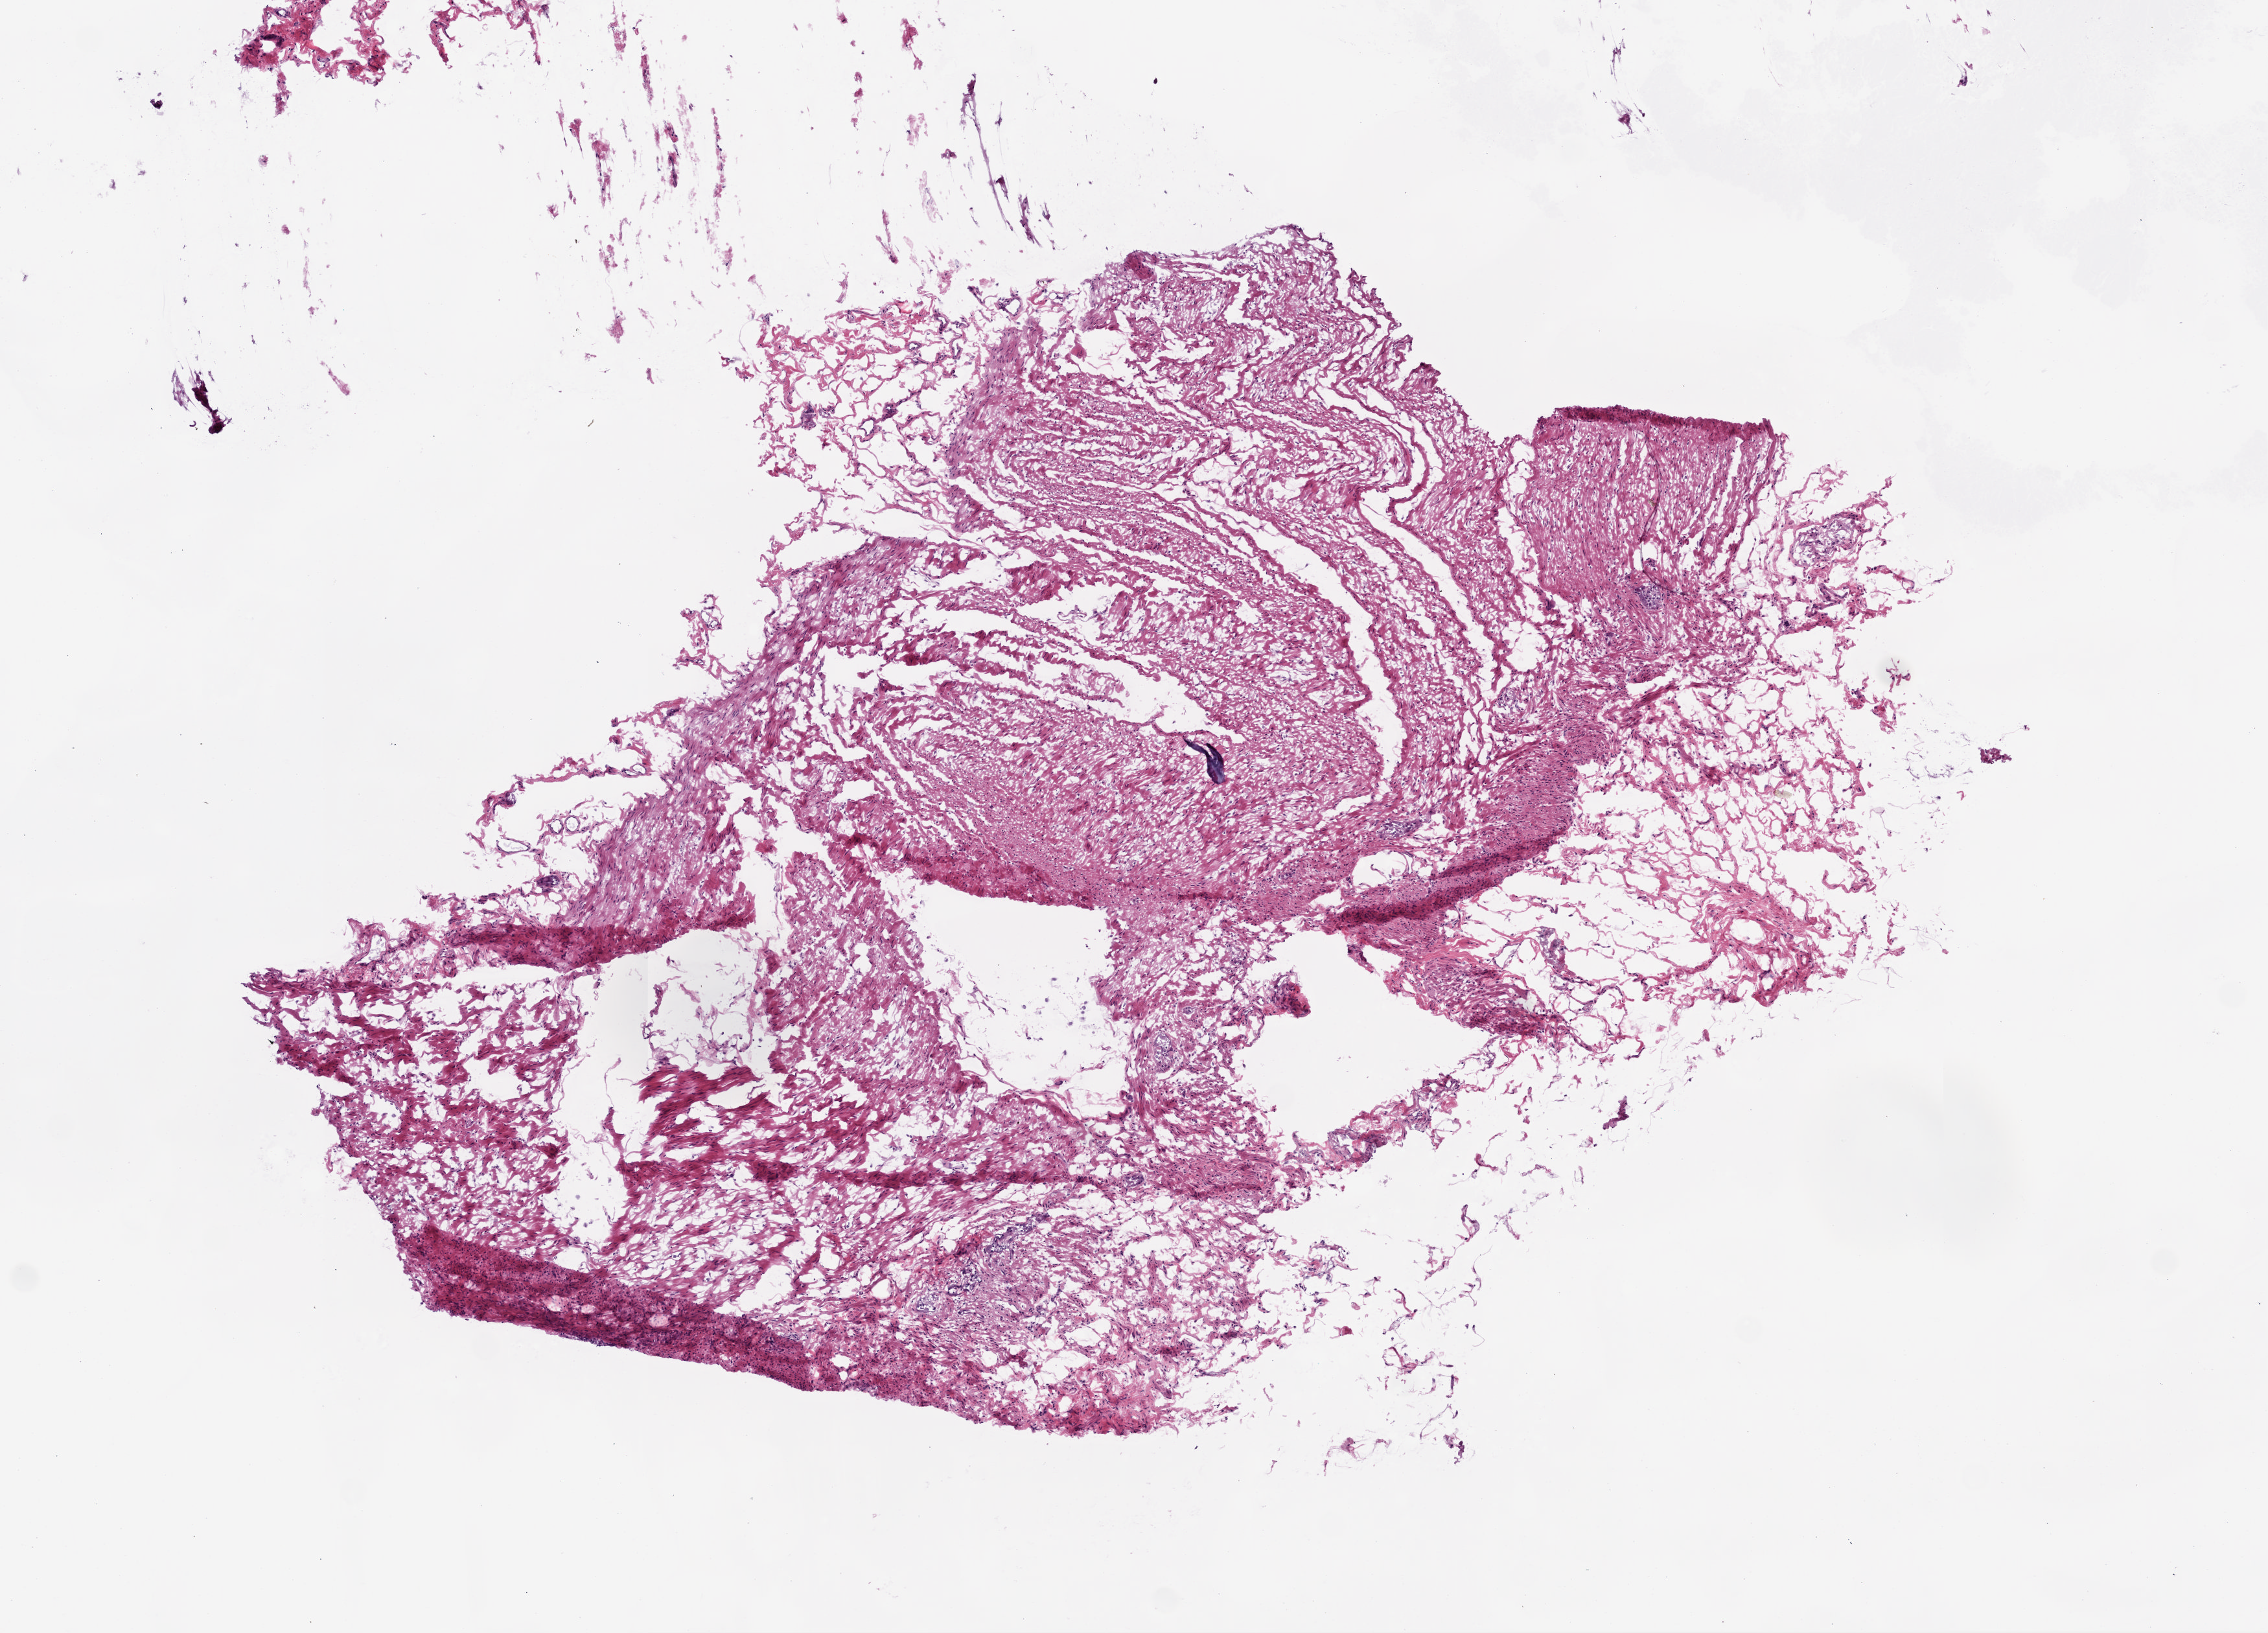
H&E whole-slide image — a low-resolution overview of the entire scanned area, about 7.0 x 5.1 mm (from a 20x scan), frozen section from the top of the tissue portion, rectum, solid tissue normal (non-tumour tissue) sample. Patient: female, age at initial diagnosis 78 years.
This section: solid tissue normal (non-tumour) sample from the same patient. Patient diagnosis: Adenocarcinoma, NOS (rectosigmoid junction).